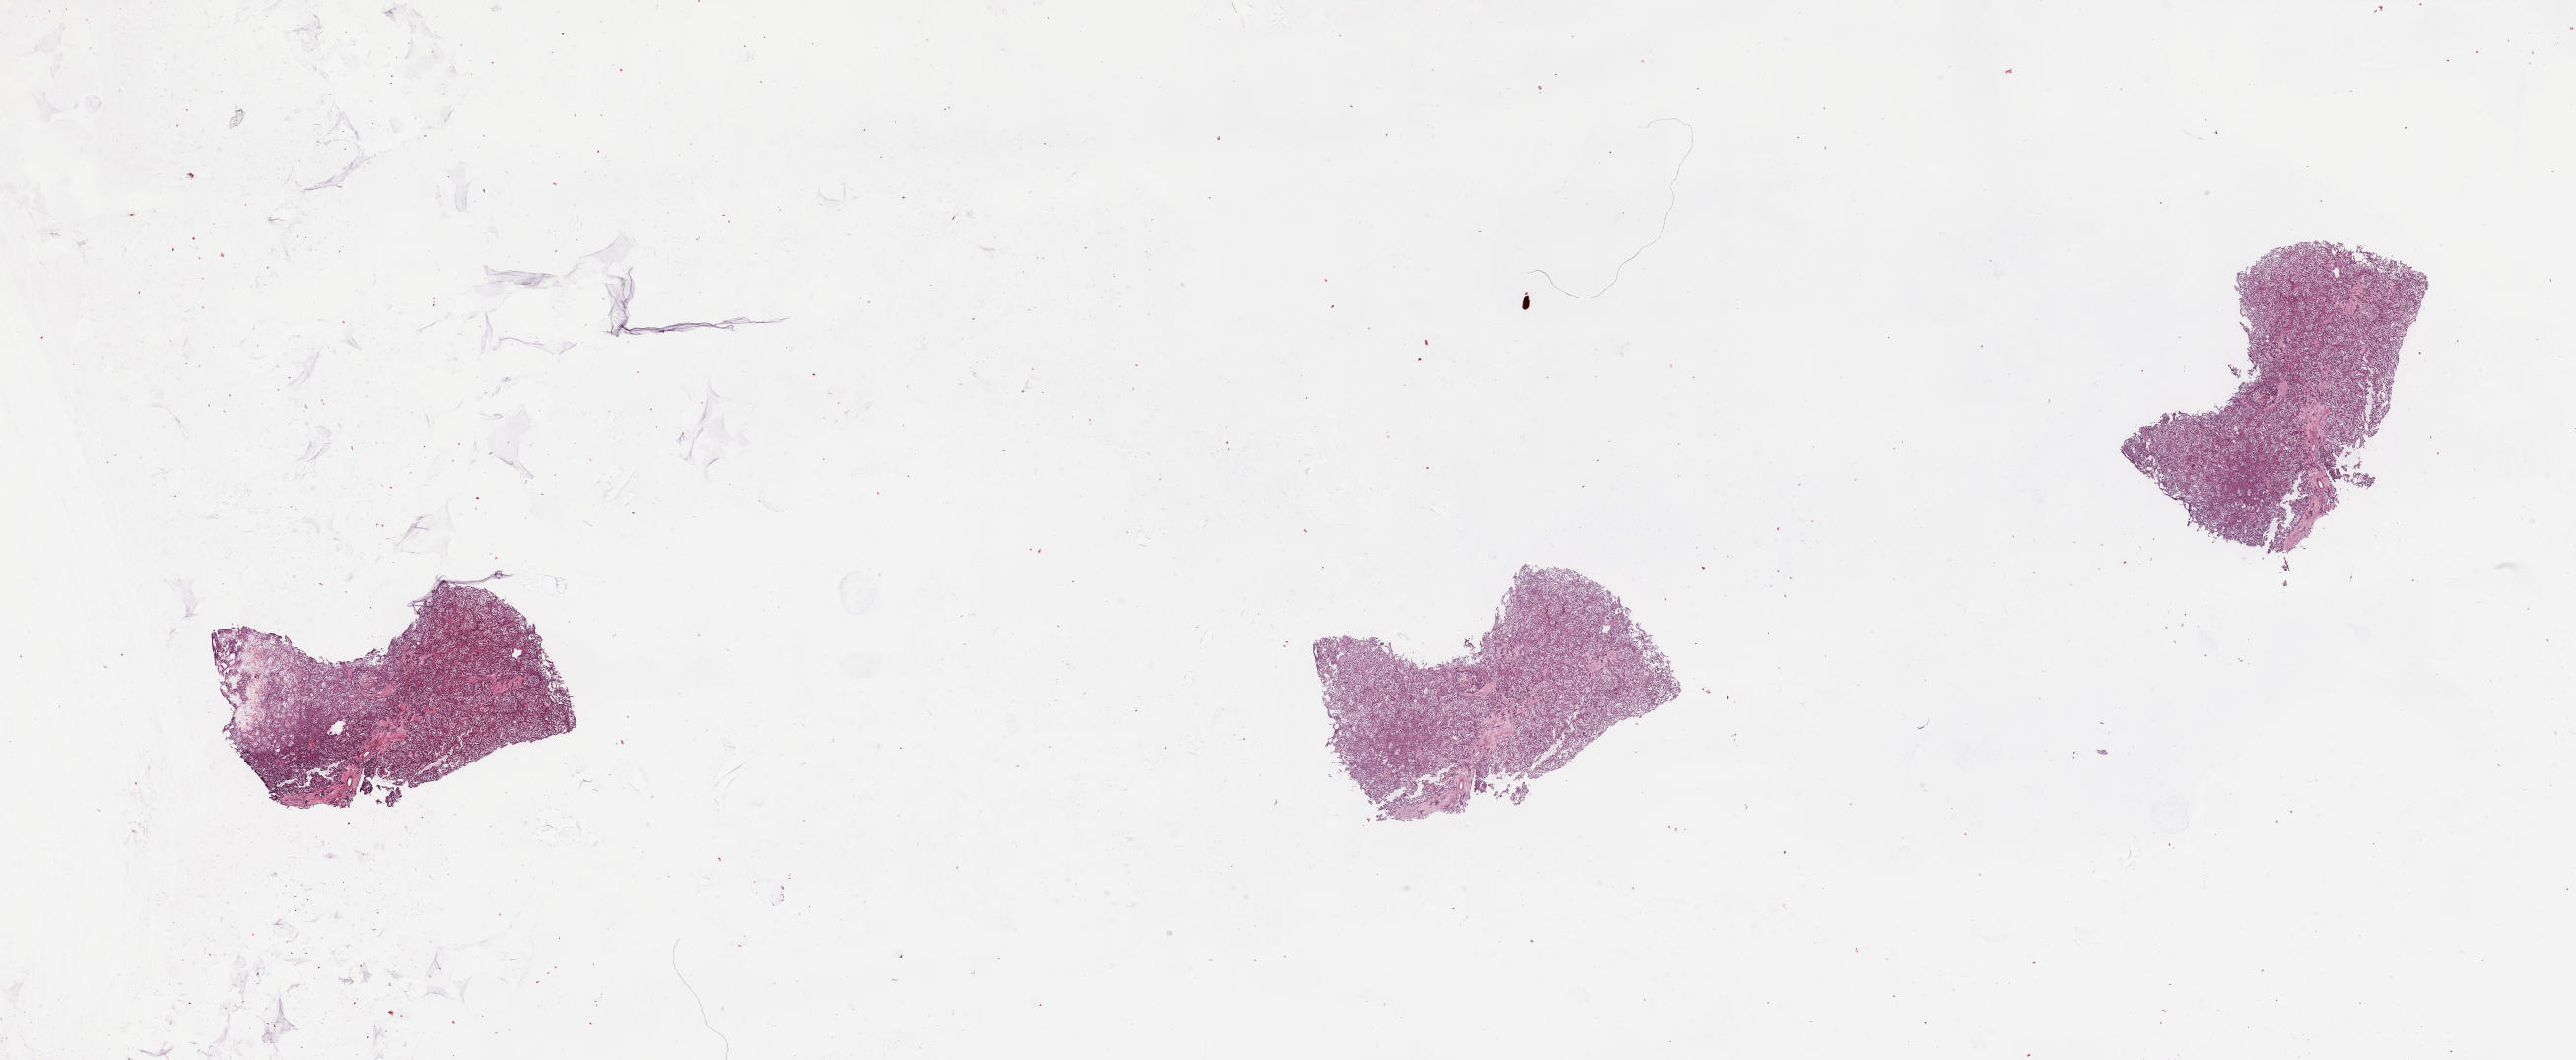
Digitized H&E-stained tissue section (whole slide) — whole scanned area (about 41.3 x 17.0 mm, from a 20x scan) shown as a low-resolution overview. Tumour tissue sample, sampled site: kidney. Patient: male, age 51 years. Histologic grade: G2 (moderately differentiated). Composition of this section per pathologist review: tumour nuclei 85%, necrosis 5%.
* AJCC pathologic stage: I
* primary tumour site (as recorded): upper pole
* histologic diagnosis: Renal cell carcinoma, NOS